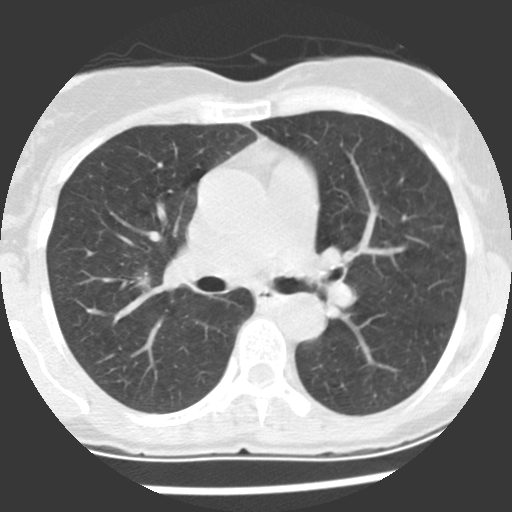
Low-dose screening chest CT, one axial slice; position 130 of 225 along the scan axis; 120 kVp; lung window (W 1500 / L -600 HU); 2.5 mm slice thickness; 512 × 512 image matrix, field of view 270 × 270 mm.
Outlined on this slice (manually delineated by an expert):
- lesion 1 (tumor, upper lobe of right lung): bounding box [x1, y1, x2, y2] px = [133, 272, 150, 289]